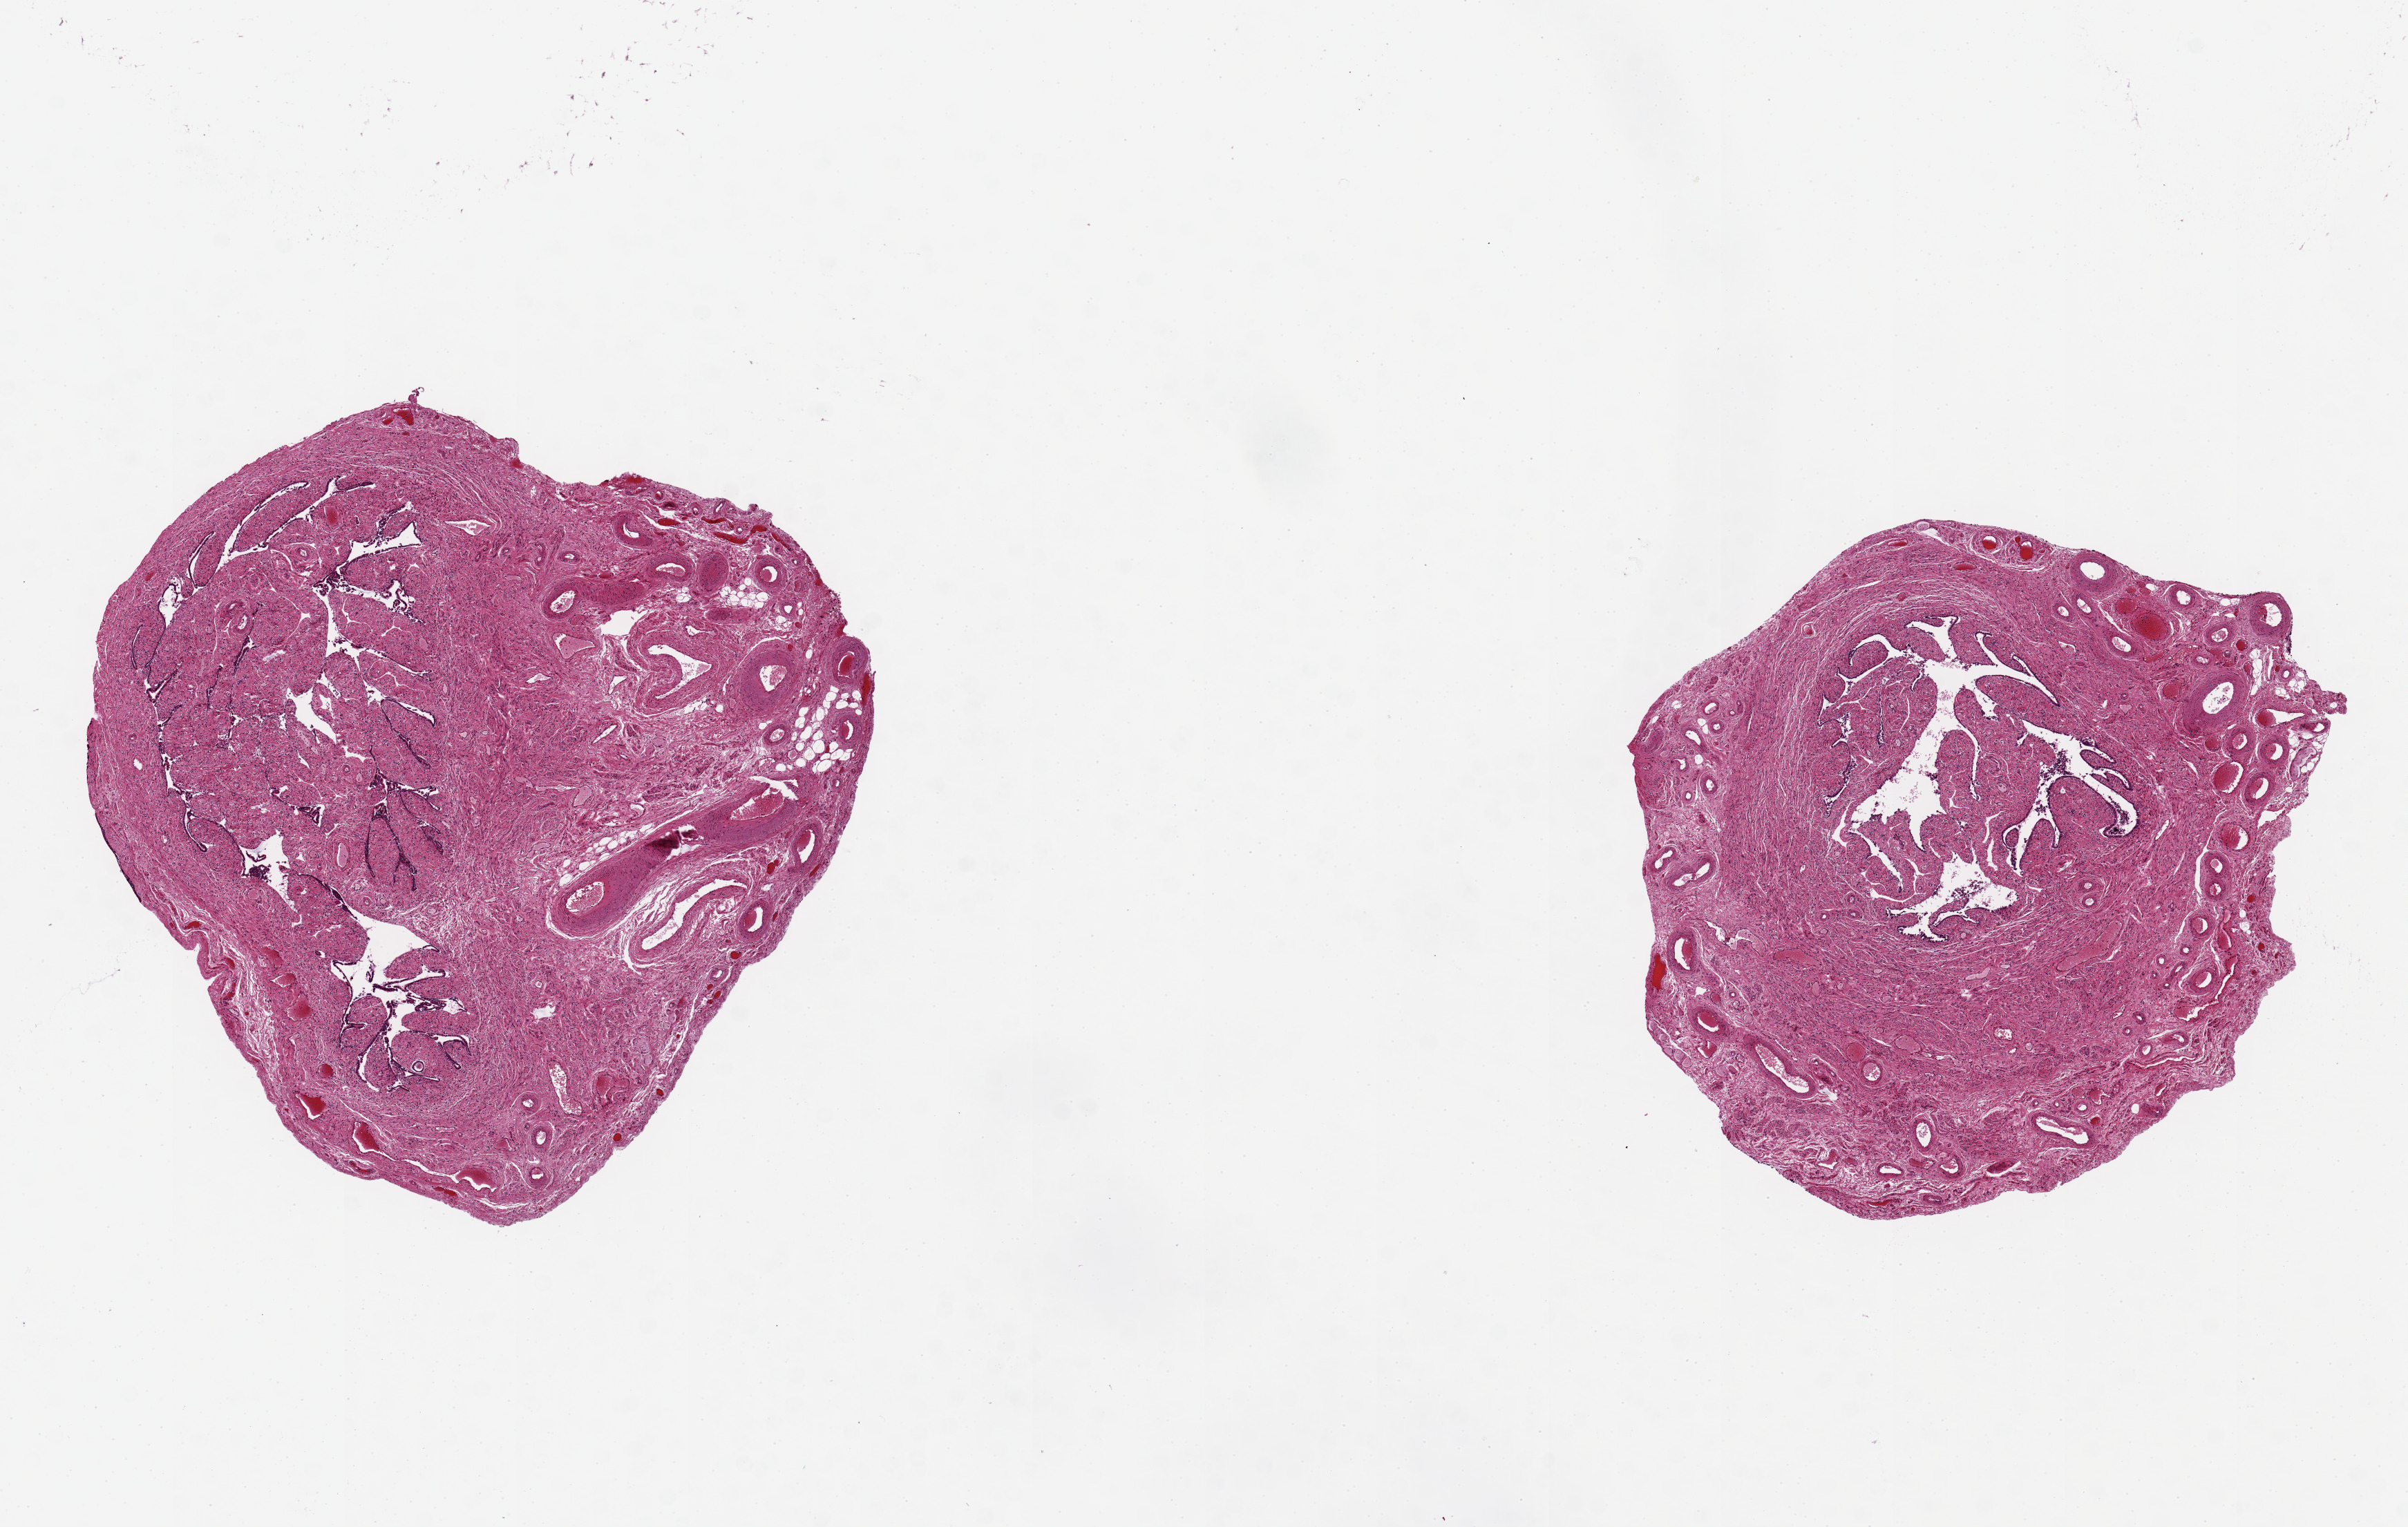
Hematoxylin and eosin (H&E) whole-slide image, shown as a low-resolution overview of the whole scanned area (about 13.8 x 8.7 mm), PAXgene-fixed paraffin-embedded (PFPE) section, section of fallopian tube (target tissue), tissue donor sample.
• reviewer comment on this tissue sample: 2 pieces 4 mm in diameter; epithelium sloughed